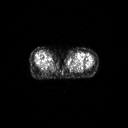
FDG PET of an extremity soft-tissue mass (from a PET/CT study), one axial slice. 3.27 mm slice thickness. 128 × 128 image matrix. Patient: female, 74 years. Case-level facts recorded for this patient, not image findings: histological type: pleomorphic leiomyosarcoma; grade: high; site of the primary tumour: left thigh.
Outlined on this slice (expert contour drawn on MRI and transferred to this co-registered scan by the dataset authors):
- gross tumour volume including surrounding oedema: bounding box (x1, y1, x2, y2) in pixels: (67, 54, 74, 59)